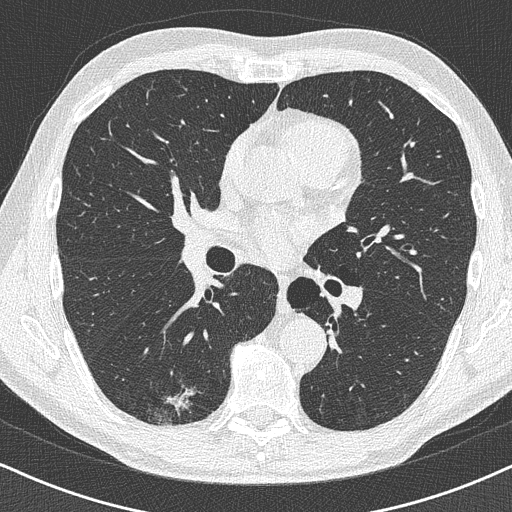
Low-dose screening chest CT, axial slice; baseline screening round; lung window (W 1500 / L -600 HU); slice 204 of 438 in the series. Male participant, aged 63 years at enrolment. Former smoker at enrolment.
Expert reader's lesion annotation, bounding box [x1, y1, x2, y2] px = [140, 376, 211, 431]. Reader record for this screening exam (exam-level; its link to the box is not recorded): non-calcified nodule or mass ≥4 mm, right lower lobe, 16 × 13 mm, poorly defined margins. Participant outcome: lung cancer diagnosed 74 days after this screen — adenocarcinoma, NOS, right lower lobe, moderately differentiated (G2), stage IA (AJCC 6th edition), 20 mm at pathology.